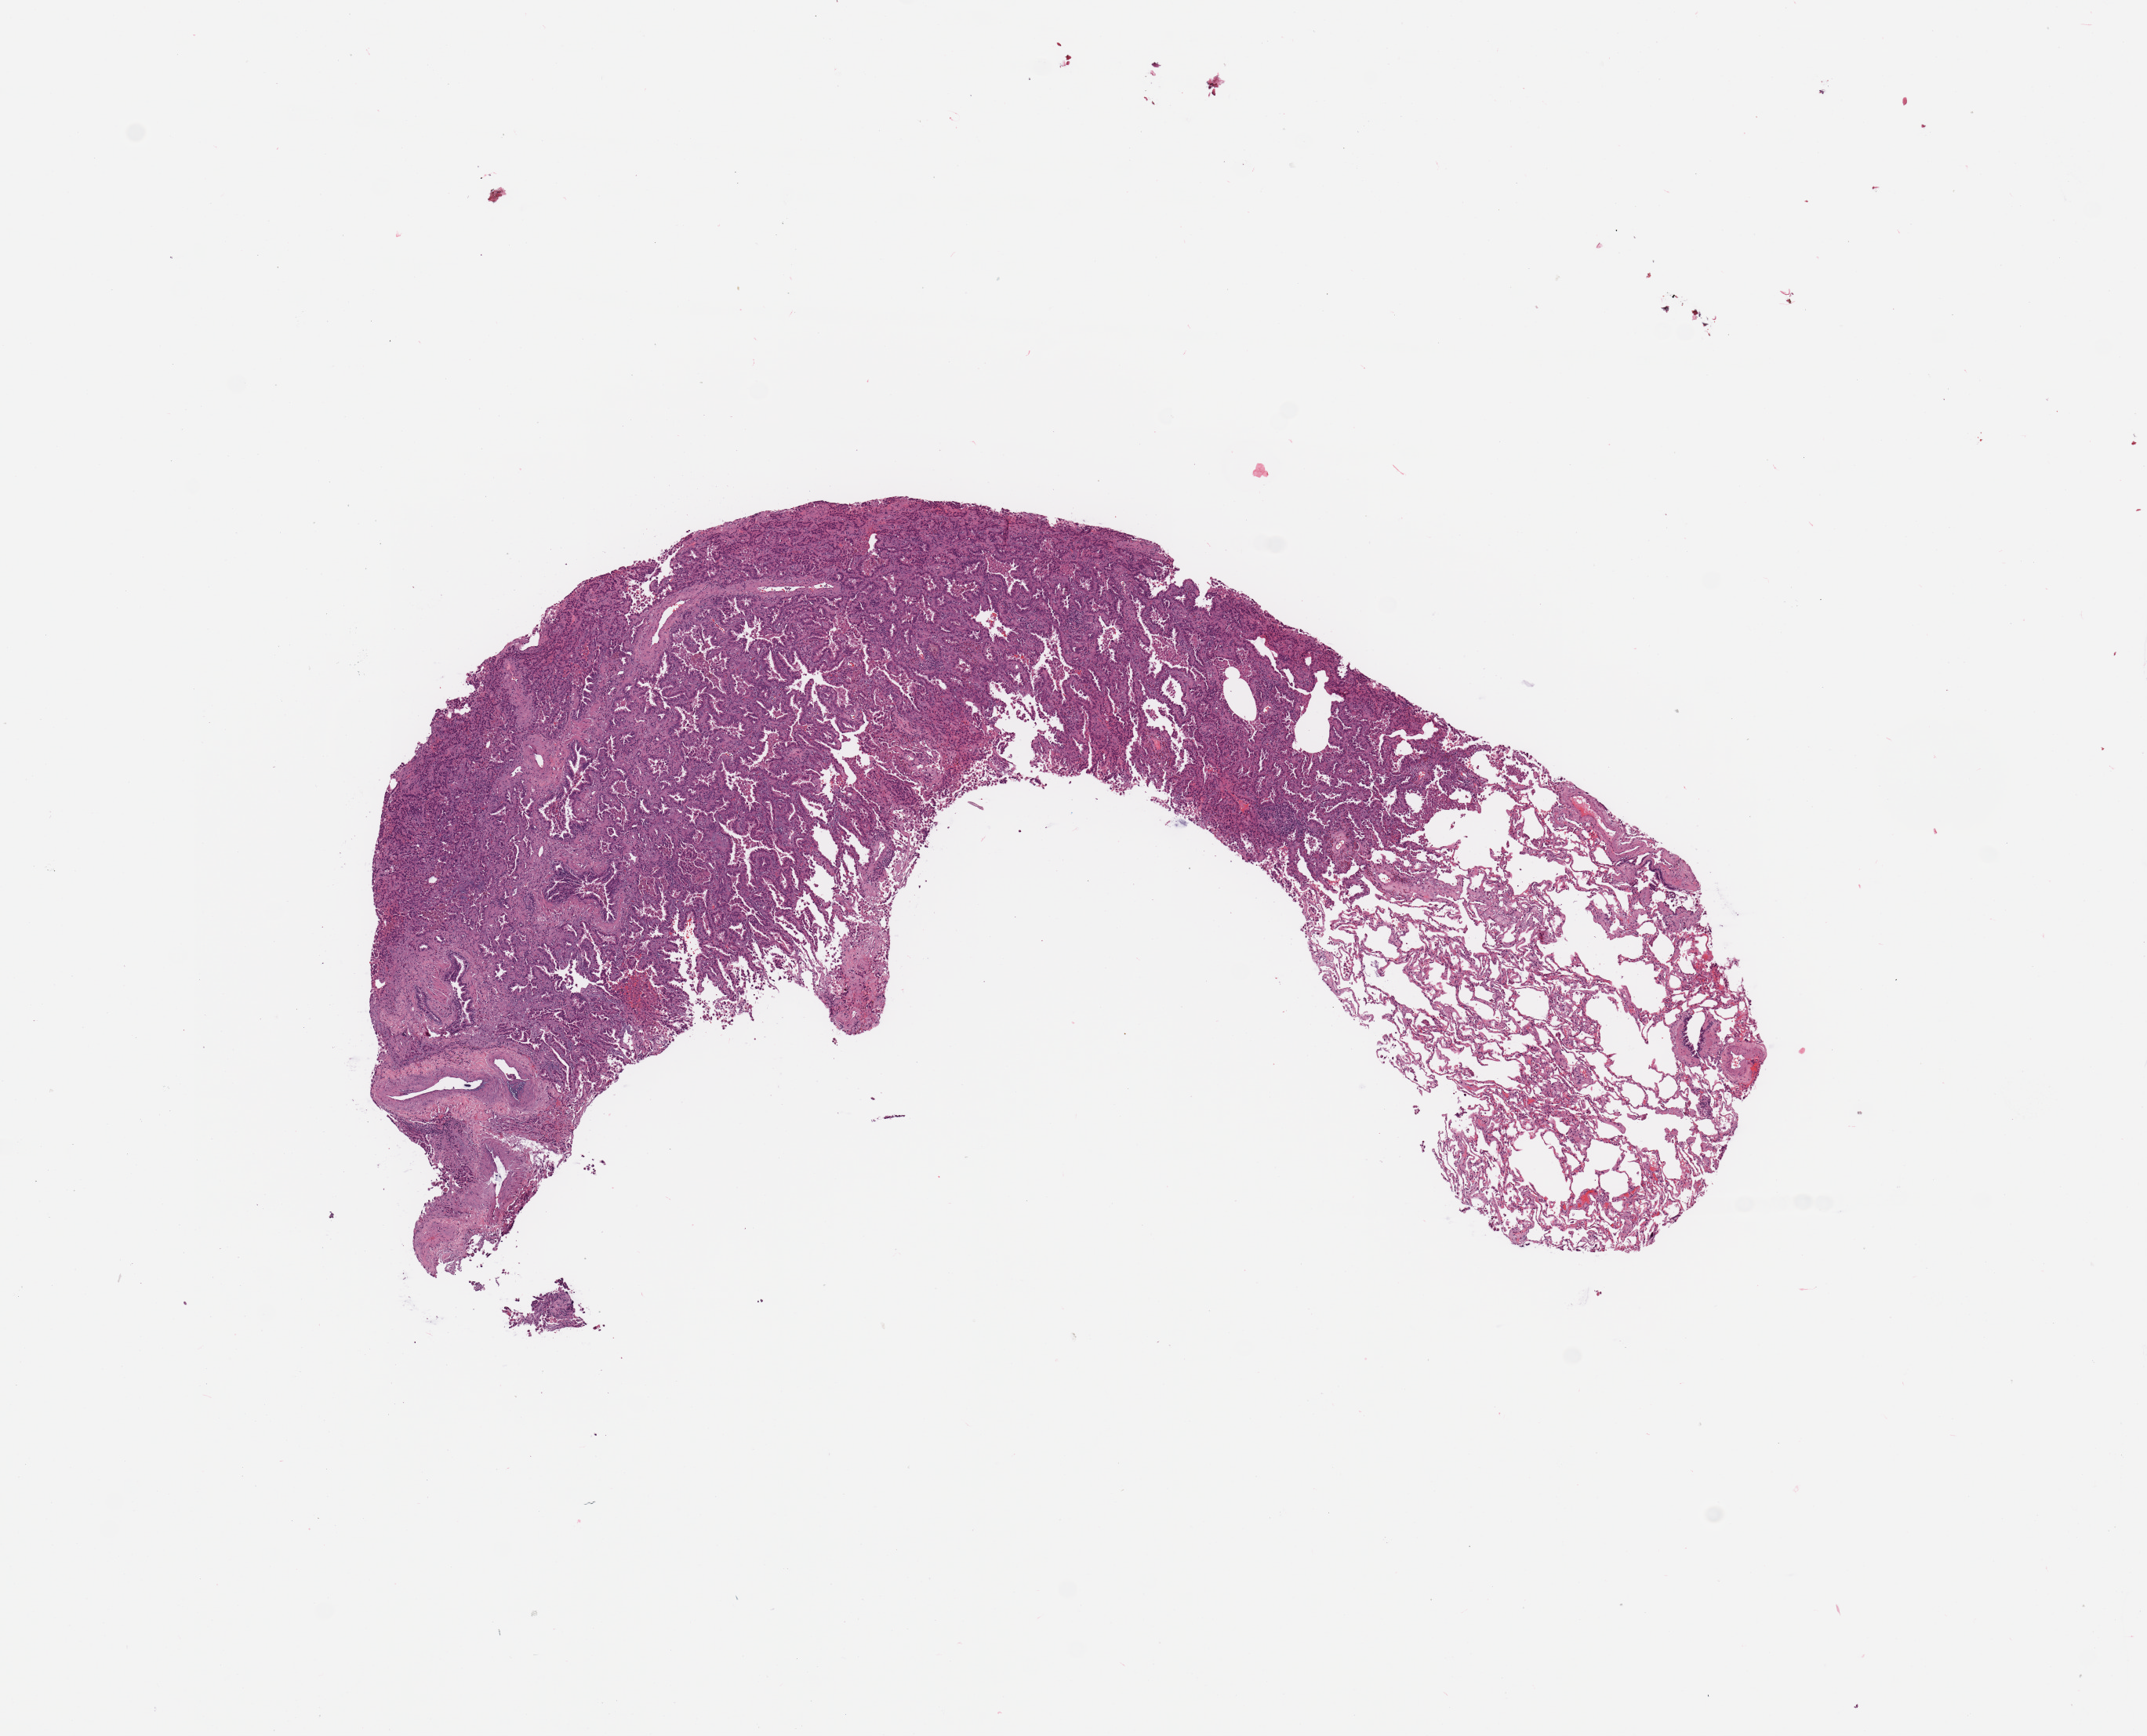
Digitized H&E-stained tissue section (whole slide), shown as a low-resolution overview of the whole scanned area (about 10.8 x 8.8 mm, from a 20x scan). Tumour tissue sample, sampled site: lung. Female, 68 y/o. Slide review estimates, as recorded: tumour nuclei 60%, necrosis 5%.
Histologic diagnosis: Adenocarcinoma, NOS.